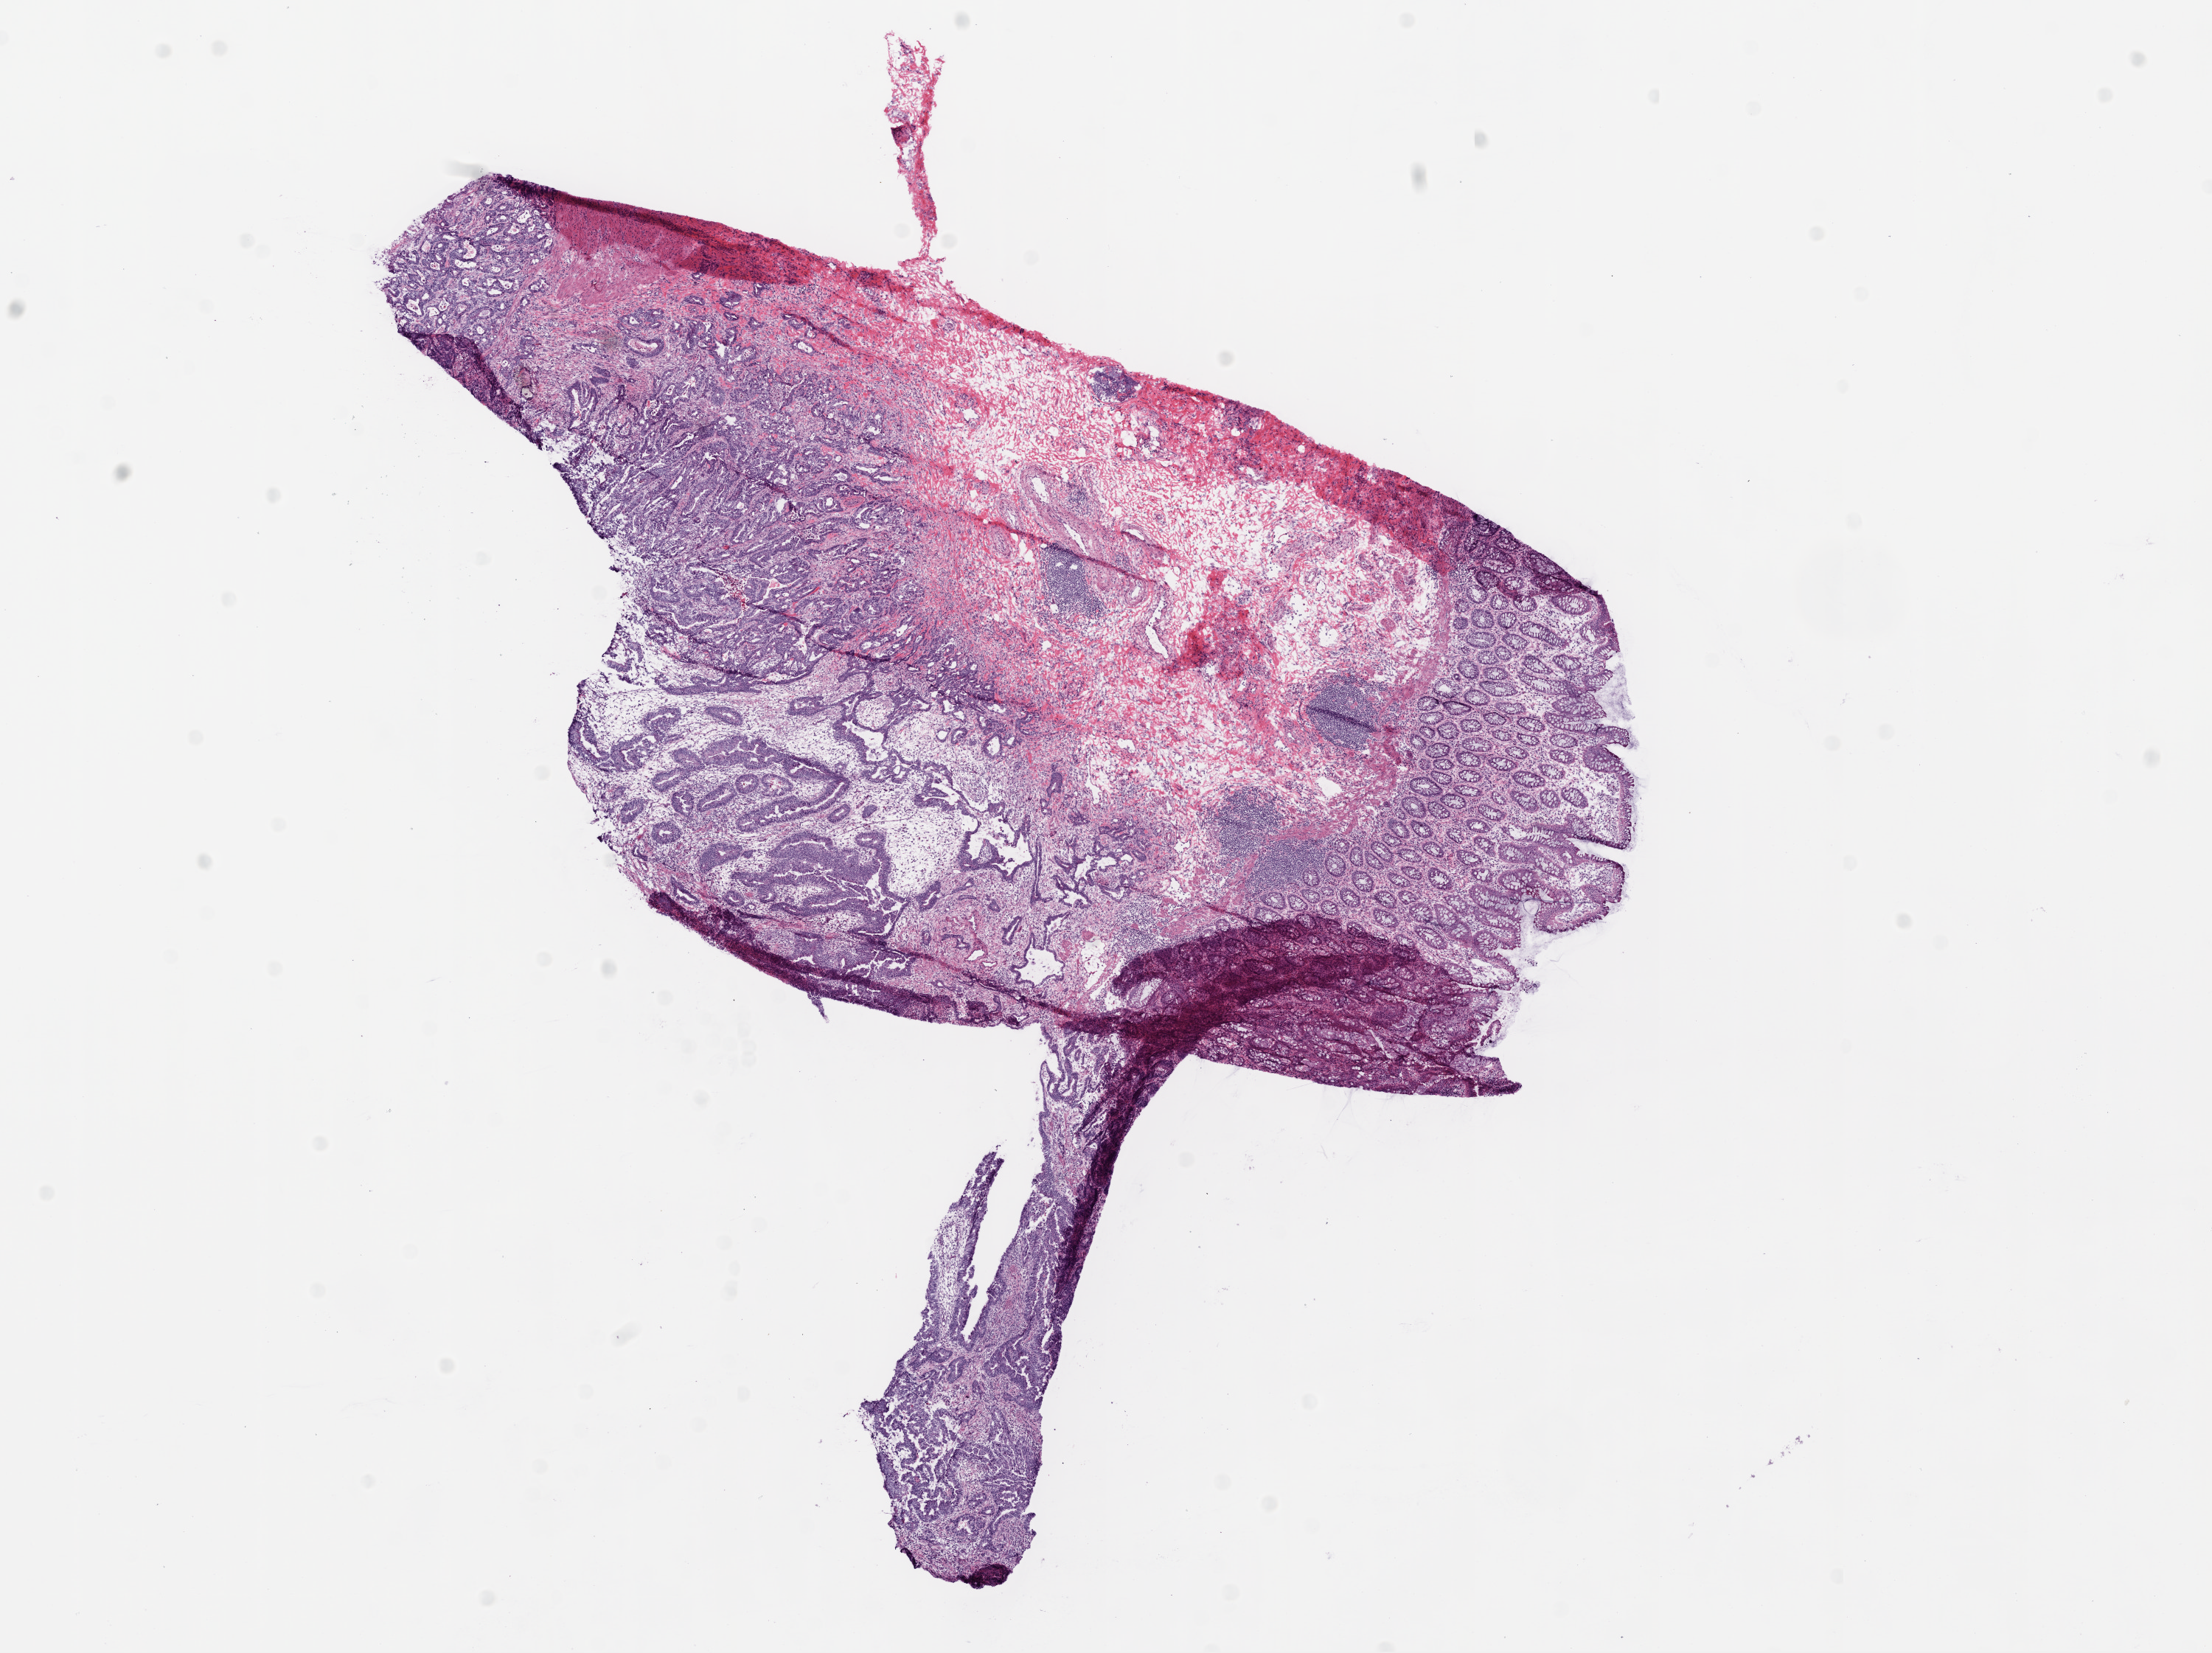
Whole-slide histology image, H&E, low-resolution overview of the scanned area, about 12.0 x 9.0 mm (from a 20x scan); frozen section from the top of the tissue portion; sample: primary tumour, rectum. Male, age 73 years at initial diagnosis. Pathologist review of this section (percent, as recorded): tumour cells 45%, tumour nuclei 50%, normal cells 45%, stromal cells 8%, necrosis 2%.
• AJCC pathologic stage: IIIB (6th edition)
• pathologic diagnosis: Adenocarcinoma, NOS